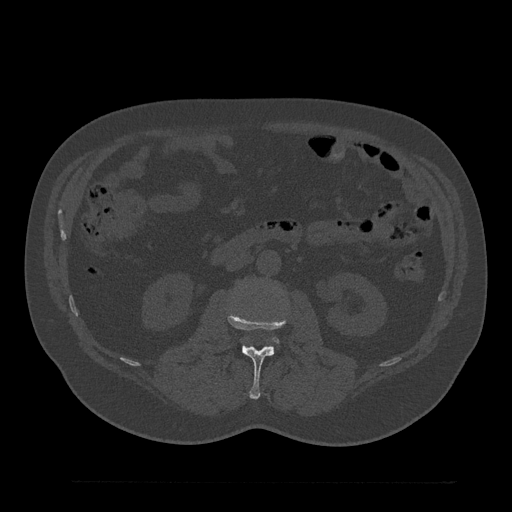
CT including the spine, one axial slice. Slice 80 of 797 in the series (ordered by position). Bone window (W 1800 / L 400 HU). 0.5 mm slice thickness. 512 × 512 image matrix, field of view 430 × 430 mm. Patient: male, 61 years. Case-level facts recorded for this patient, not image findings: primary cancer: prostate.
Outlined on this slice (semi-automatic segmentation, software-assisted and operator-edited):
- L2 vertebra: bounding box [x1, y1, x2, y2] px = [227, 311, 288, 400]
- L3 vertebra: [274, 338, 276, 341]